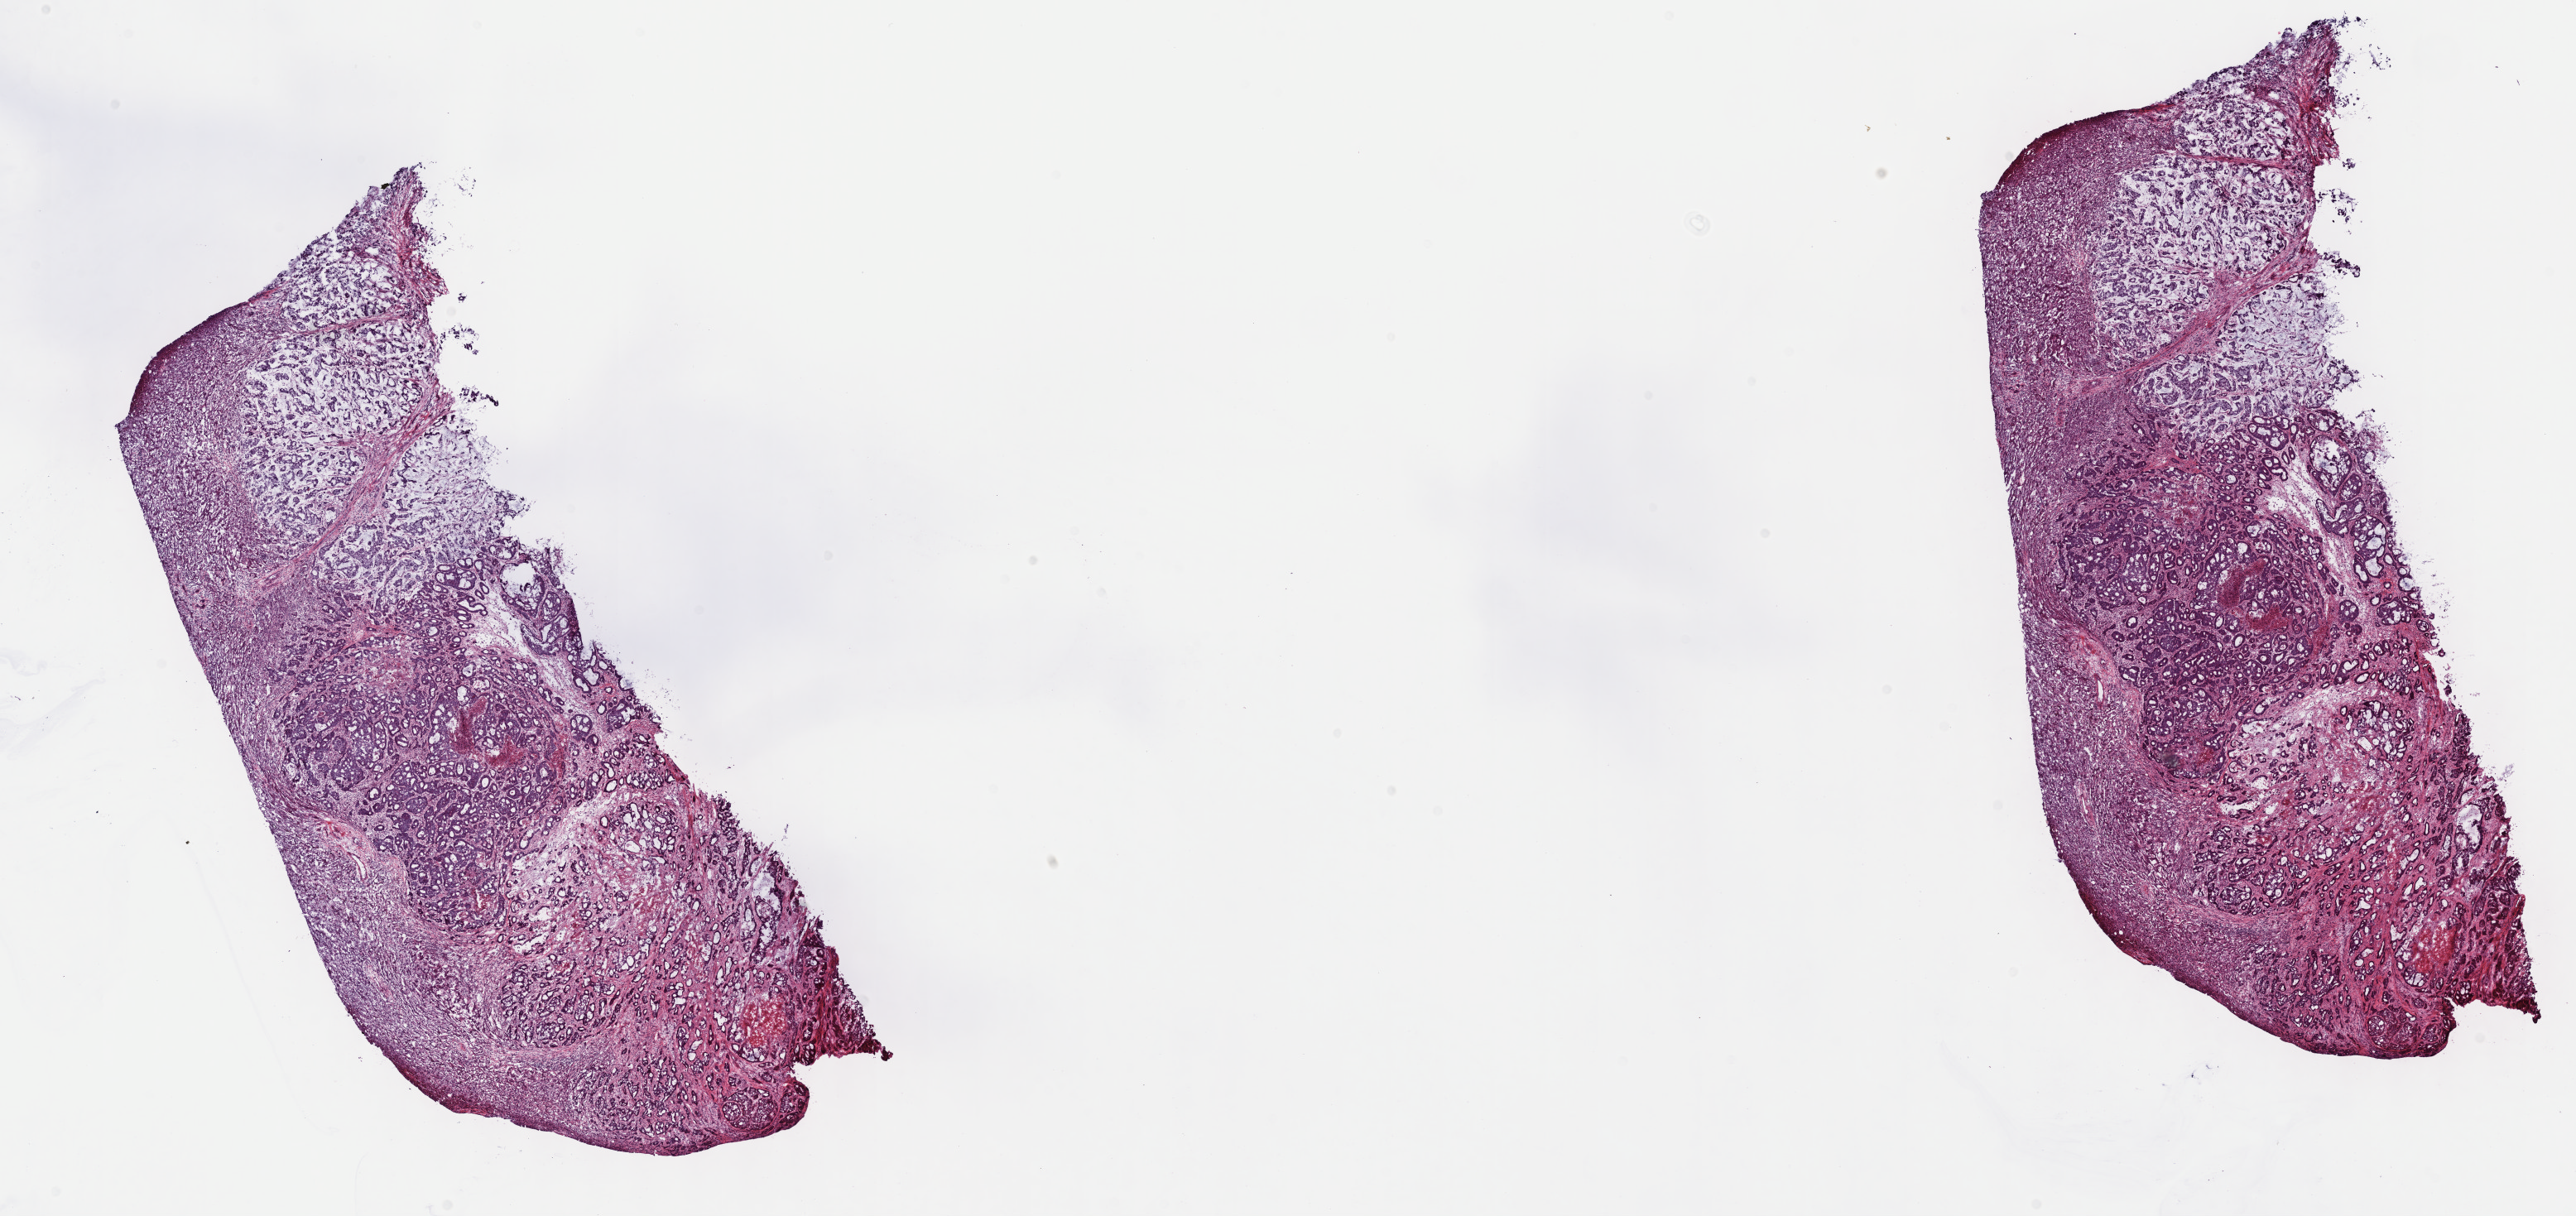
Digitized H&E tissue section (whole slide) — low-resolution overview of the scanned area, about 25.2 x 11.9 mm (slide scanned at 40x); frozen section; primary tumour sample from the bile duct. Male, age 67 years at initial diagnosis. Histologic grade: G4 (undifferentiated). Composition of this section per pathologist review: tumour cells 63%, tumour nuclei 75%, normal cells 0%, stromal cells 30%, necrosis 7%. Infiltration values recorded for this section: lymphocyte infiltration 22%, monocyte infiltration 2%, neutrophil infiltration 2%.
Diagnosis: Cholangiocarcinoma (extrahepatic bile duct). AJCC pathologic stage: IVB (7th edition).